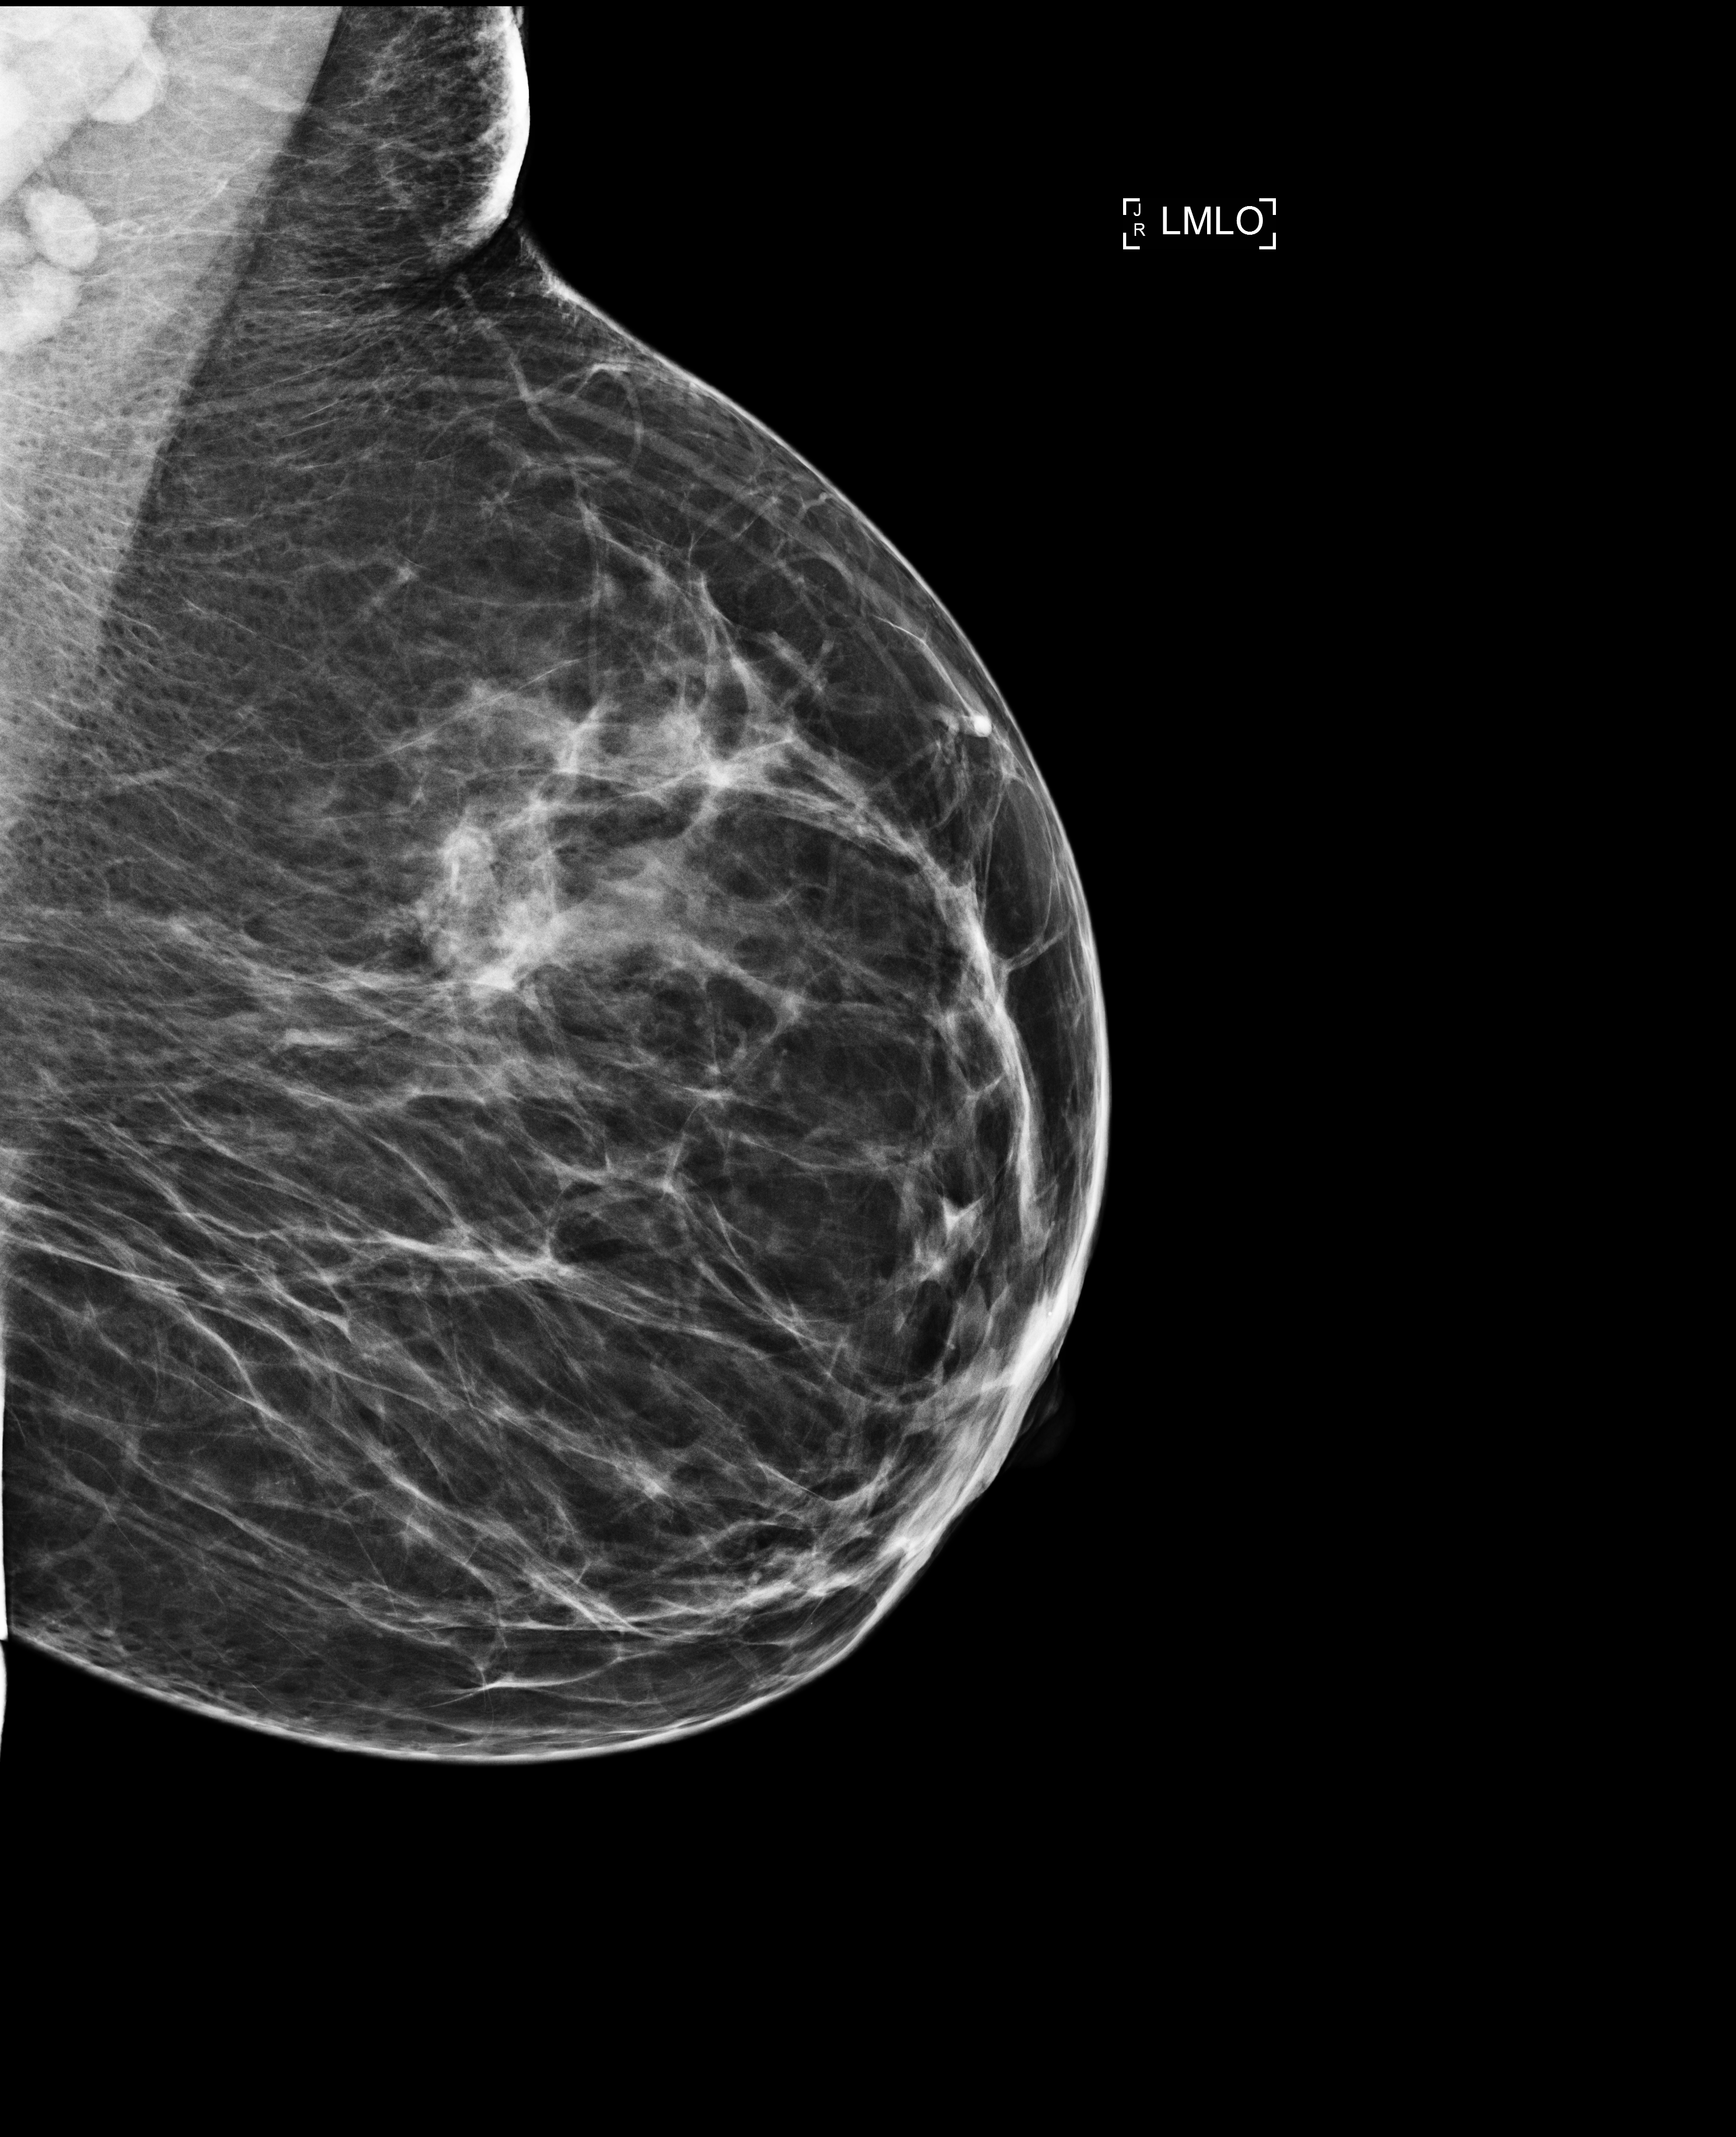
Full-field digital mammogram (FFDM), left breast, mediolateral oblique (MLO) view, annual screening mammography examination, system: Selenia Dimensions. Patient: female, 50 years.
- BI-RADS breast density category at the screening exam (both breasts, scale 1–4): 3
- final BI-RADS assessment for this screening round (tomosynthesis exam, both breasts): category 1
- recall: no recall after this screen